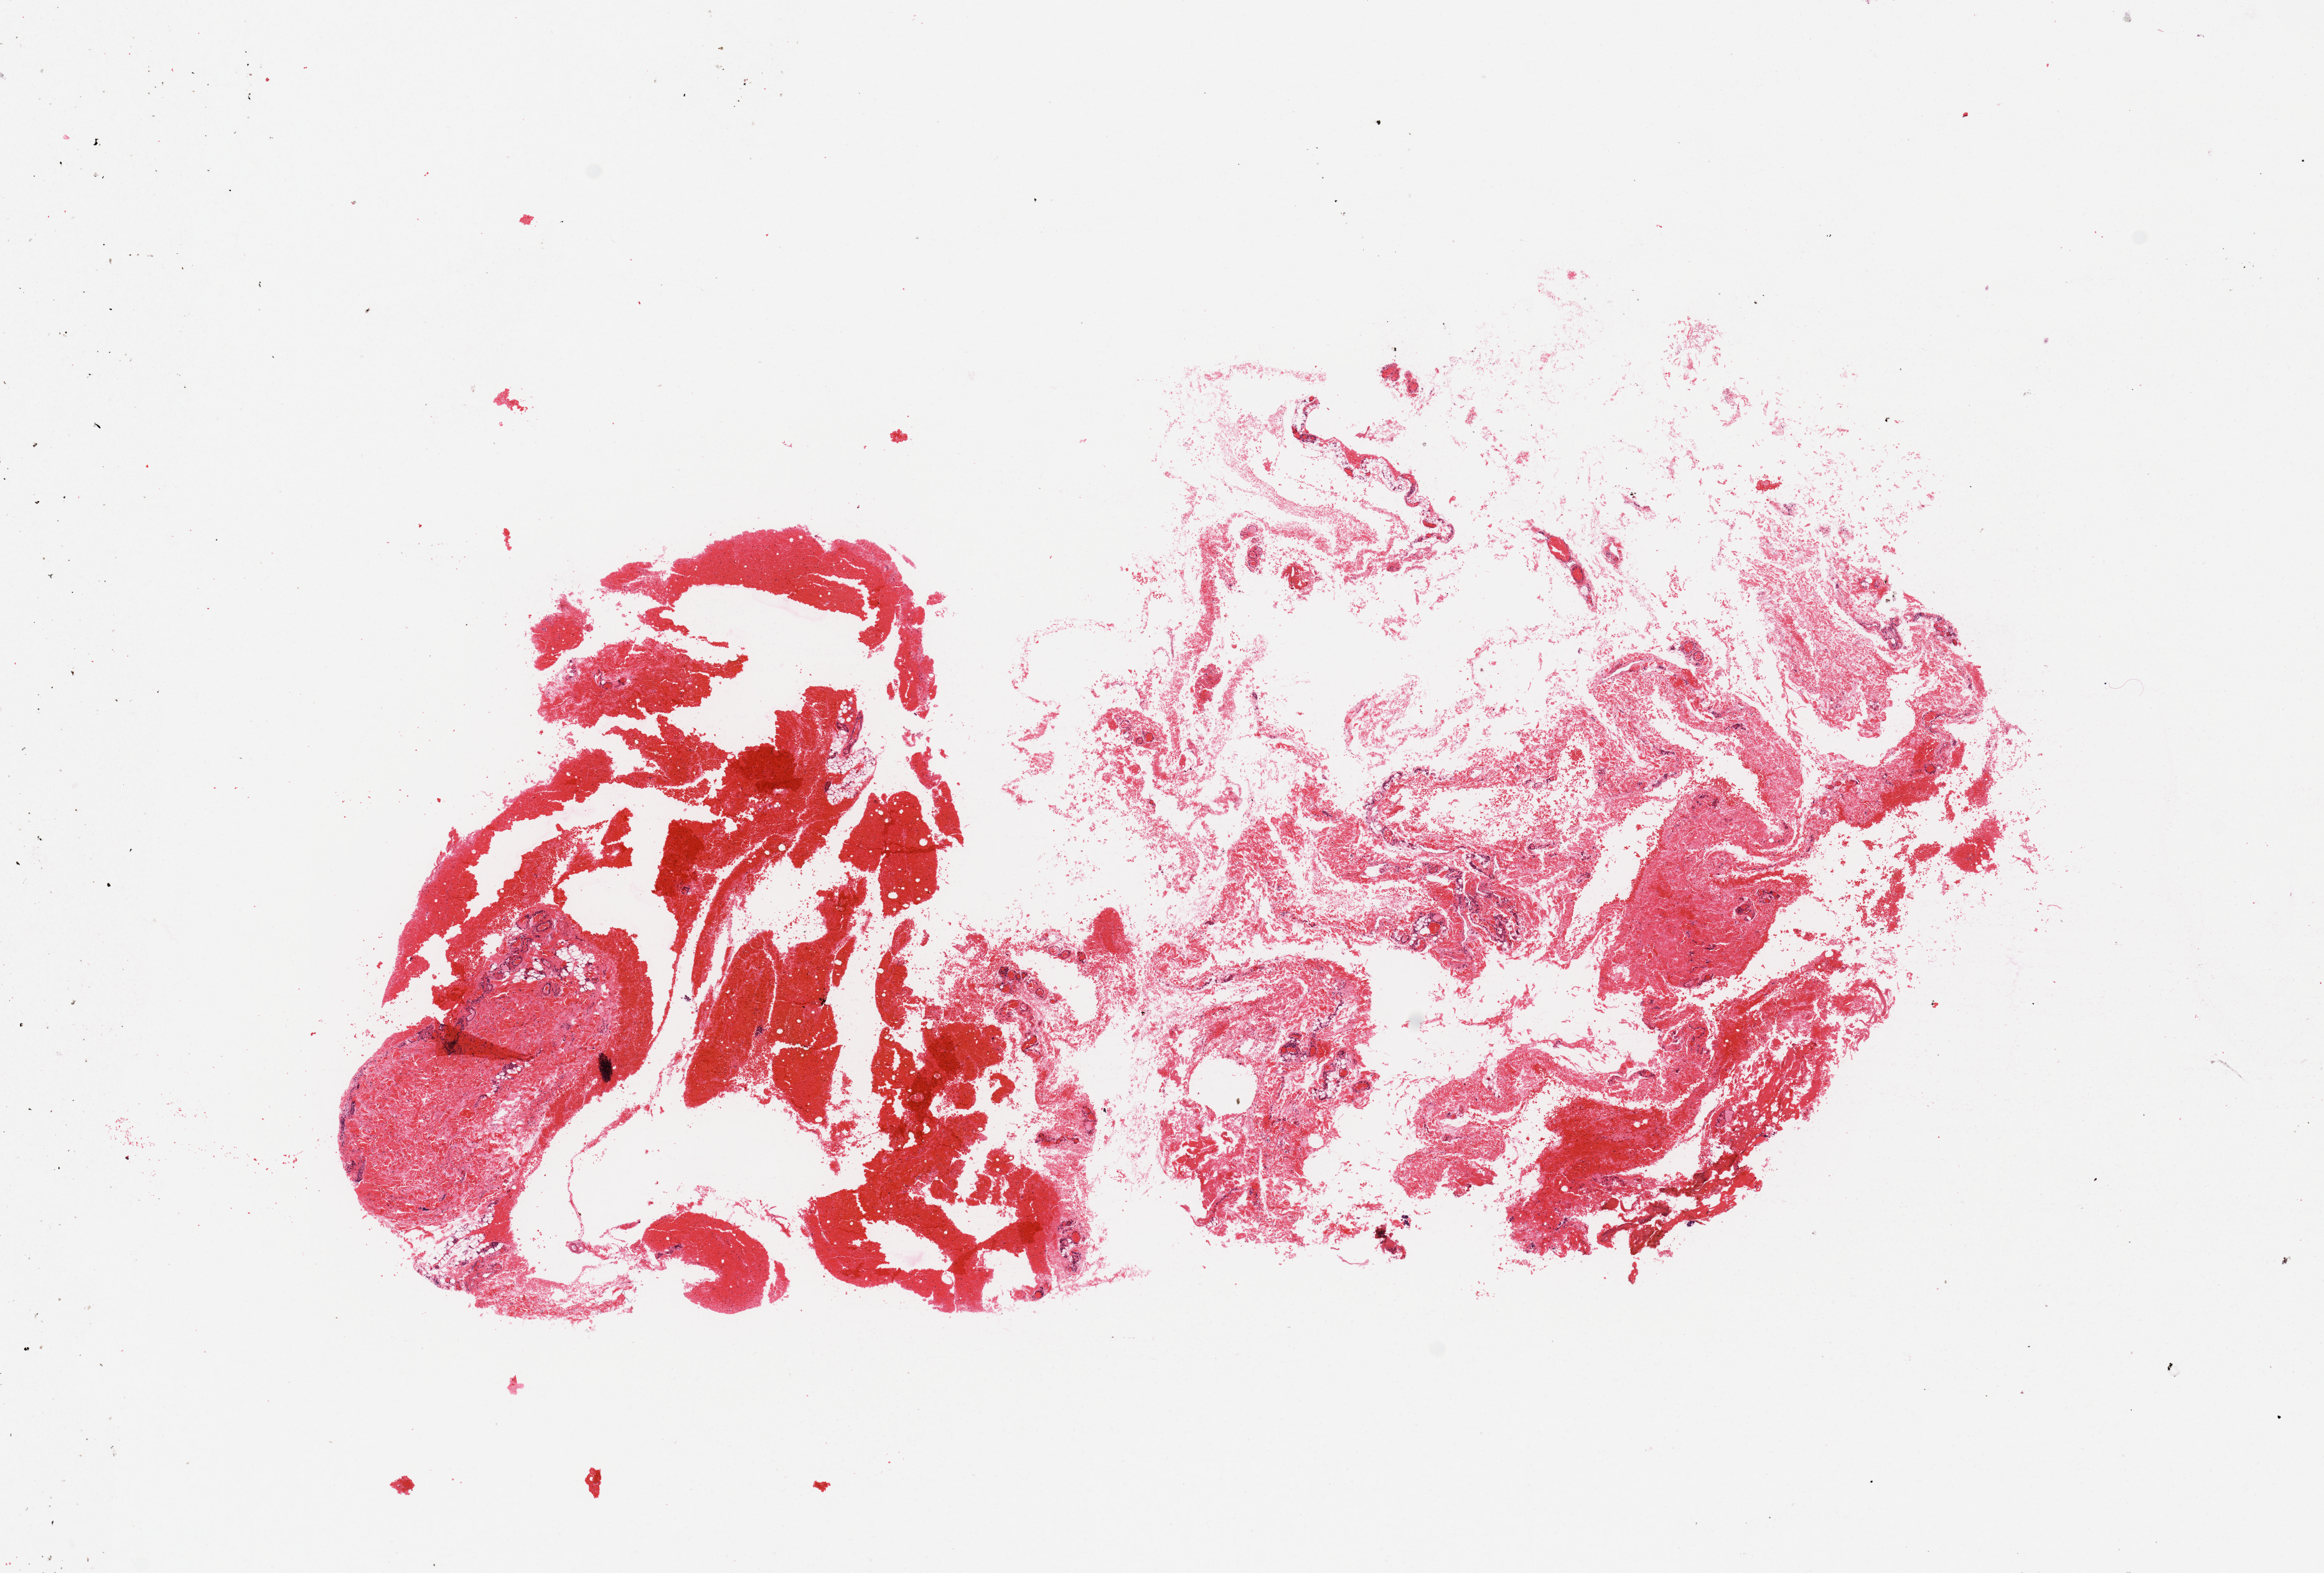
Whole-slide histology image, H&E, a low-resolution overview of the entire scanned area, about 14.8 x 10.0 mm. Normal (non-tumour) tissue sample. 56-year-old male patient.
- this section: normal (non-tumour) tissue from the same patient
- patient diagnosis (cohort enrolment): sarcoma (site not recorded at cohort level)